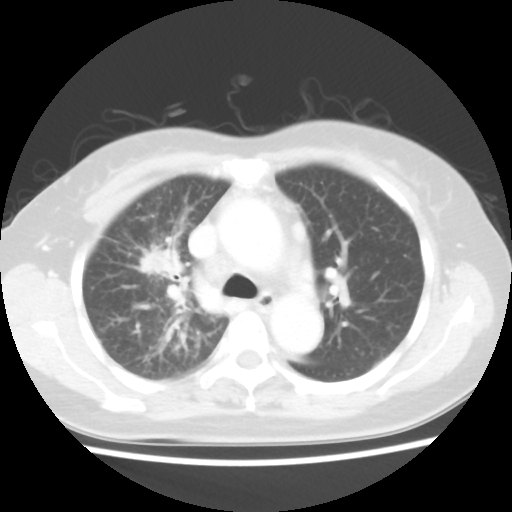
Chest CT, one axial slice; reconstruction kernel STANDARD; lung window (W 1500 / L -600 HU); 5 mm slice thickness; 512 × 512 image matrix. Patient: female, 55 years. From the clinical record (not read from this slice): clinical TNM (as recorded): T1b N3 M1a.
Annotated regions visible in this slice (rectangle marked by the reading radiologist):
- lung tumour (recorded histology: adenocarcinoma): bounding box [x1, y1, x2, y2] px = [140, 250, 183, 282]